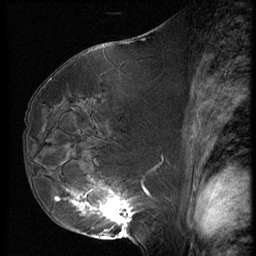
Breast MRI (dynamic contrast-enhanced), one sagittal slice; position 35 of 62 along the scan axis; 3 images stored at this slice position (order not interpretable as contrast timing); 1.5 T; TE 4.2 ms, TR 9 ms; 2.5 mm slice thickness; 256 × 256 image matrix. Patient: female, 50 years. From the clinical record (not read from this slice): setting: breast cancer imaged before/during neoadjuvant chemotherapy; receptor status: HR-positive, HER2-negative.
Outlined on this slice (semi-automatically segmented with operator editing):
- analysis volume of interest (the breast-tissue region the enhancement analysis was run in; not a lesion): box from (x=59, y=125) to (x=139, y=238) px
- tumour enhancement mask (voxels above the 140 % enhancement threshold inside the analysis volume of interest): (x=59, y=190)–(x=136, y=222)